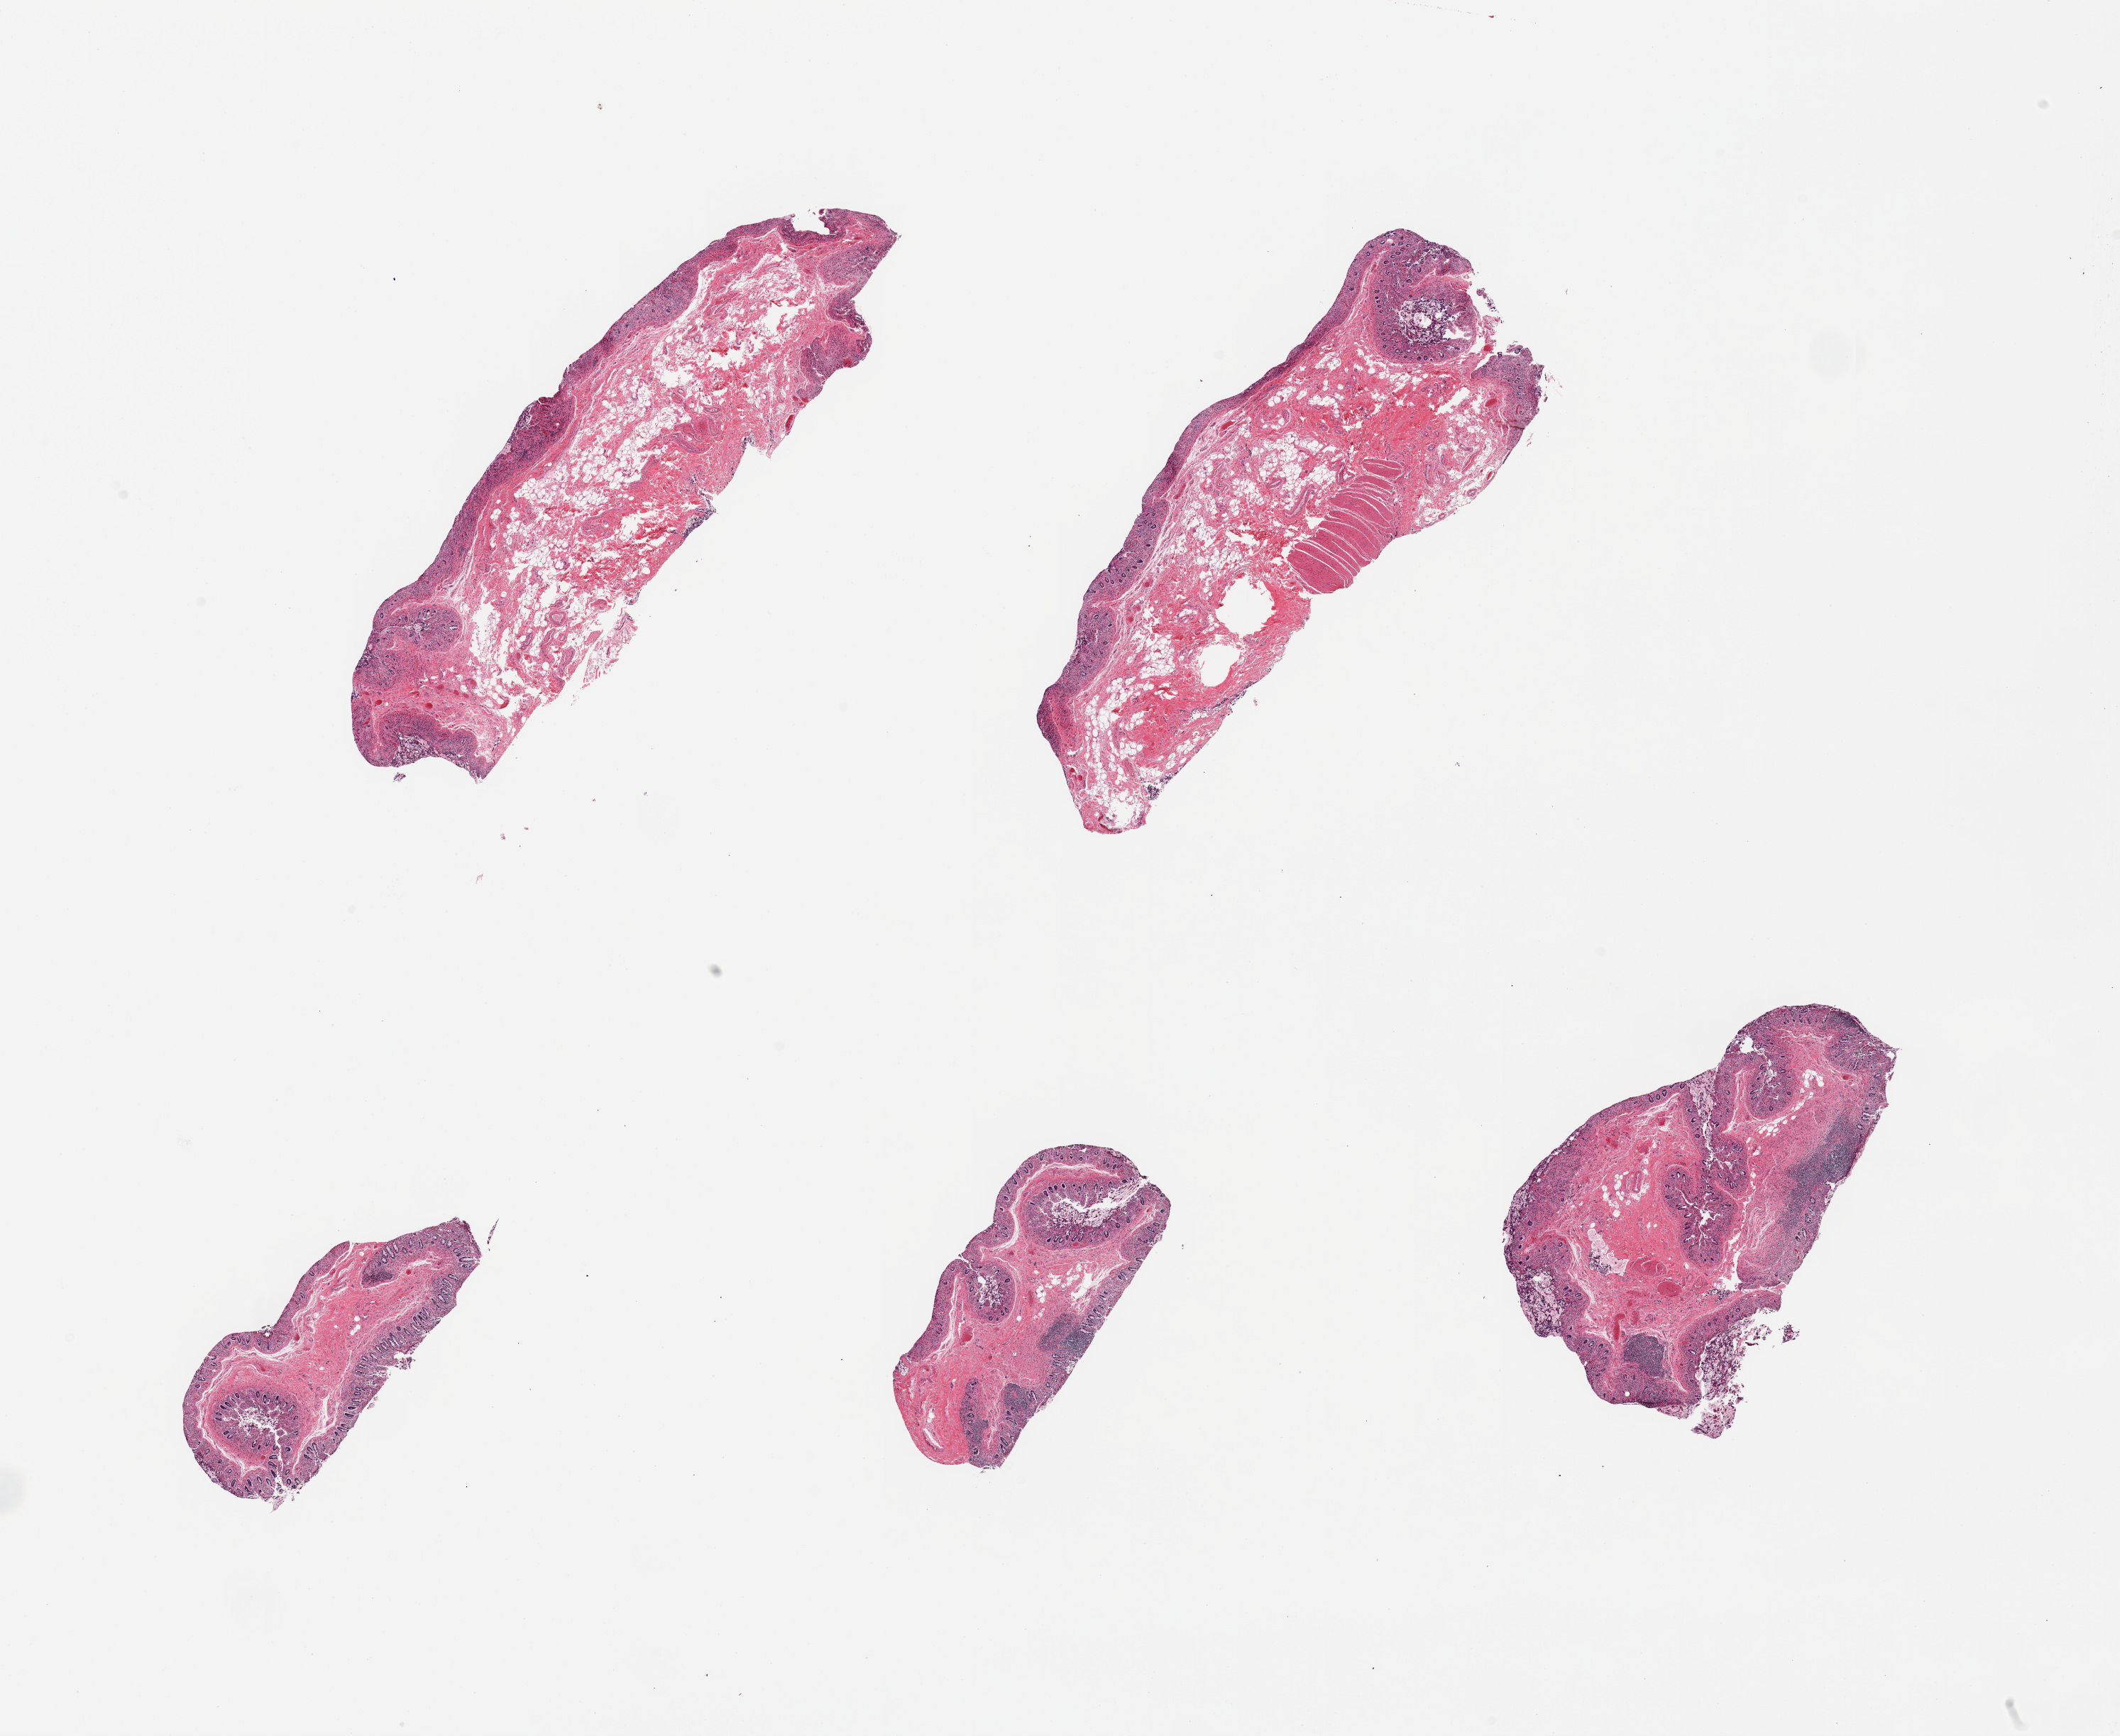
H&E whole-slide image — whole scanned area (about 23.6 x 19.3 mm) shown as a low-resolution overview; PAXgene-fixed paraffin-embedded (PFPE) section; section of ileum (target tissue); donor tissue sample. Male donor.
- pathologist's review note for this sample: 5 pieces; predominantly moderately and severely autolyzed mucosa with only minimal lymphoid tissue and few foci of muscularis (not target)